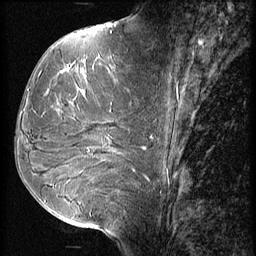
Breast MRI (dynamic contrast-enhanced), one sagittal slice; position 28 of 56 along the scan axis; 3 images stored at this slice position (order not interpretable as contrast timing); 1.5 T; TE 4.2 ms, TR 9 ms; 2.5 mm slice thickness; 256 × 256 image matrix. Patient: female, 51 years. Case-level facts recorded for this patient, not image findings: setting: breast cancer imaged before/during neoadjuvant chemotherapy; receptor status: HR-positive, HER2-negative.
Outlined on this slice (semi-automatic segmentation, software-assisted and operator-edited):
- analysis volume of interest (the breast-tissue region the enhancement analysis was run in; not a lesion): bounding box (x1, y1, x2, y2) in pixels: (23, 56, 156, 165)
- tumour enhancement mask (voxels above the 140 % enhancement threshold inside the analysis volume of interest): (62, 70, 110, 73)